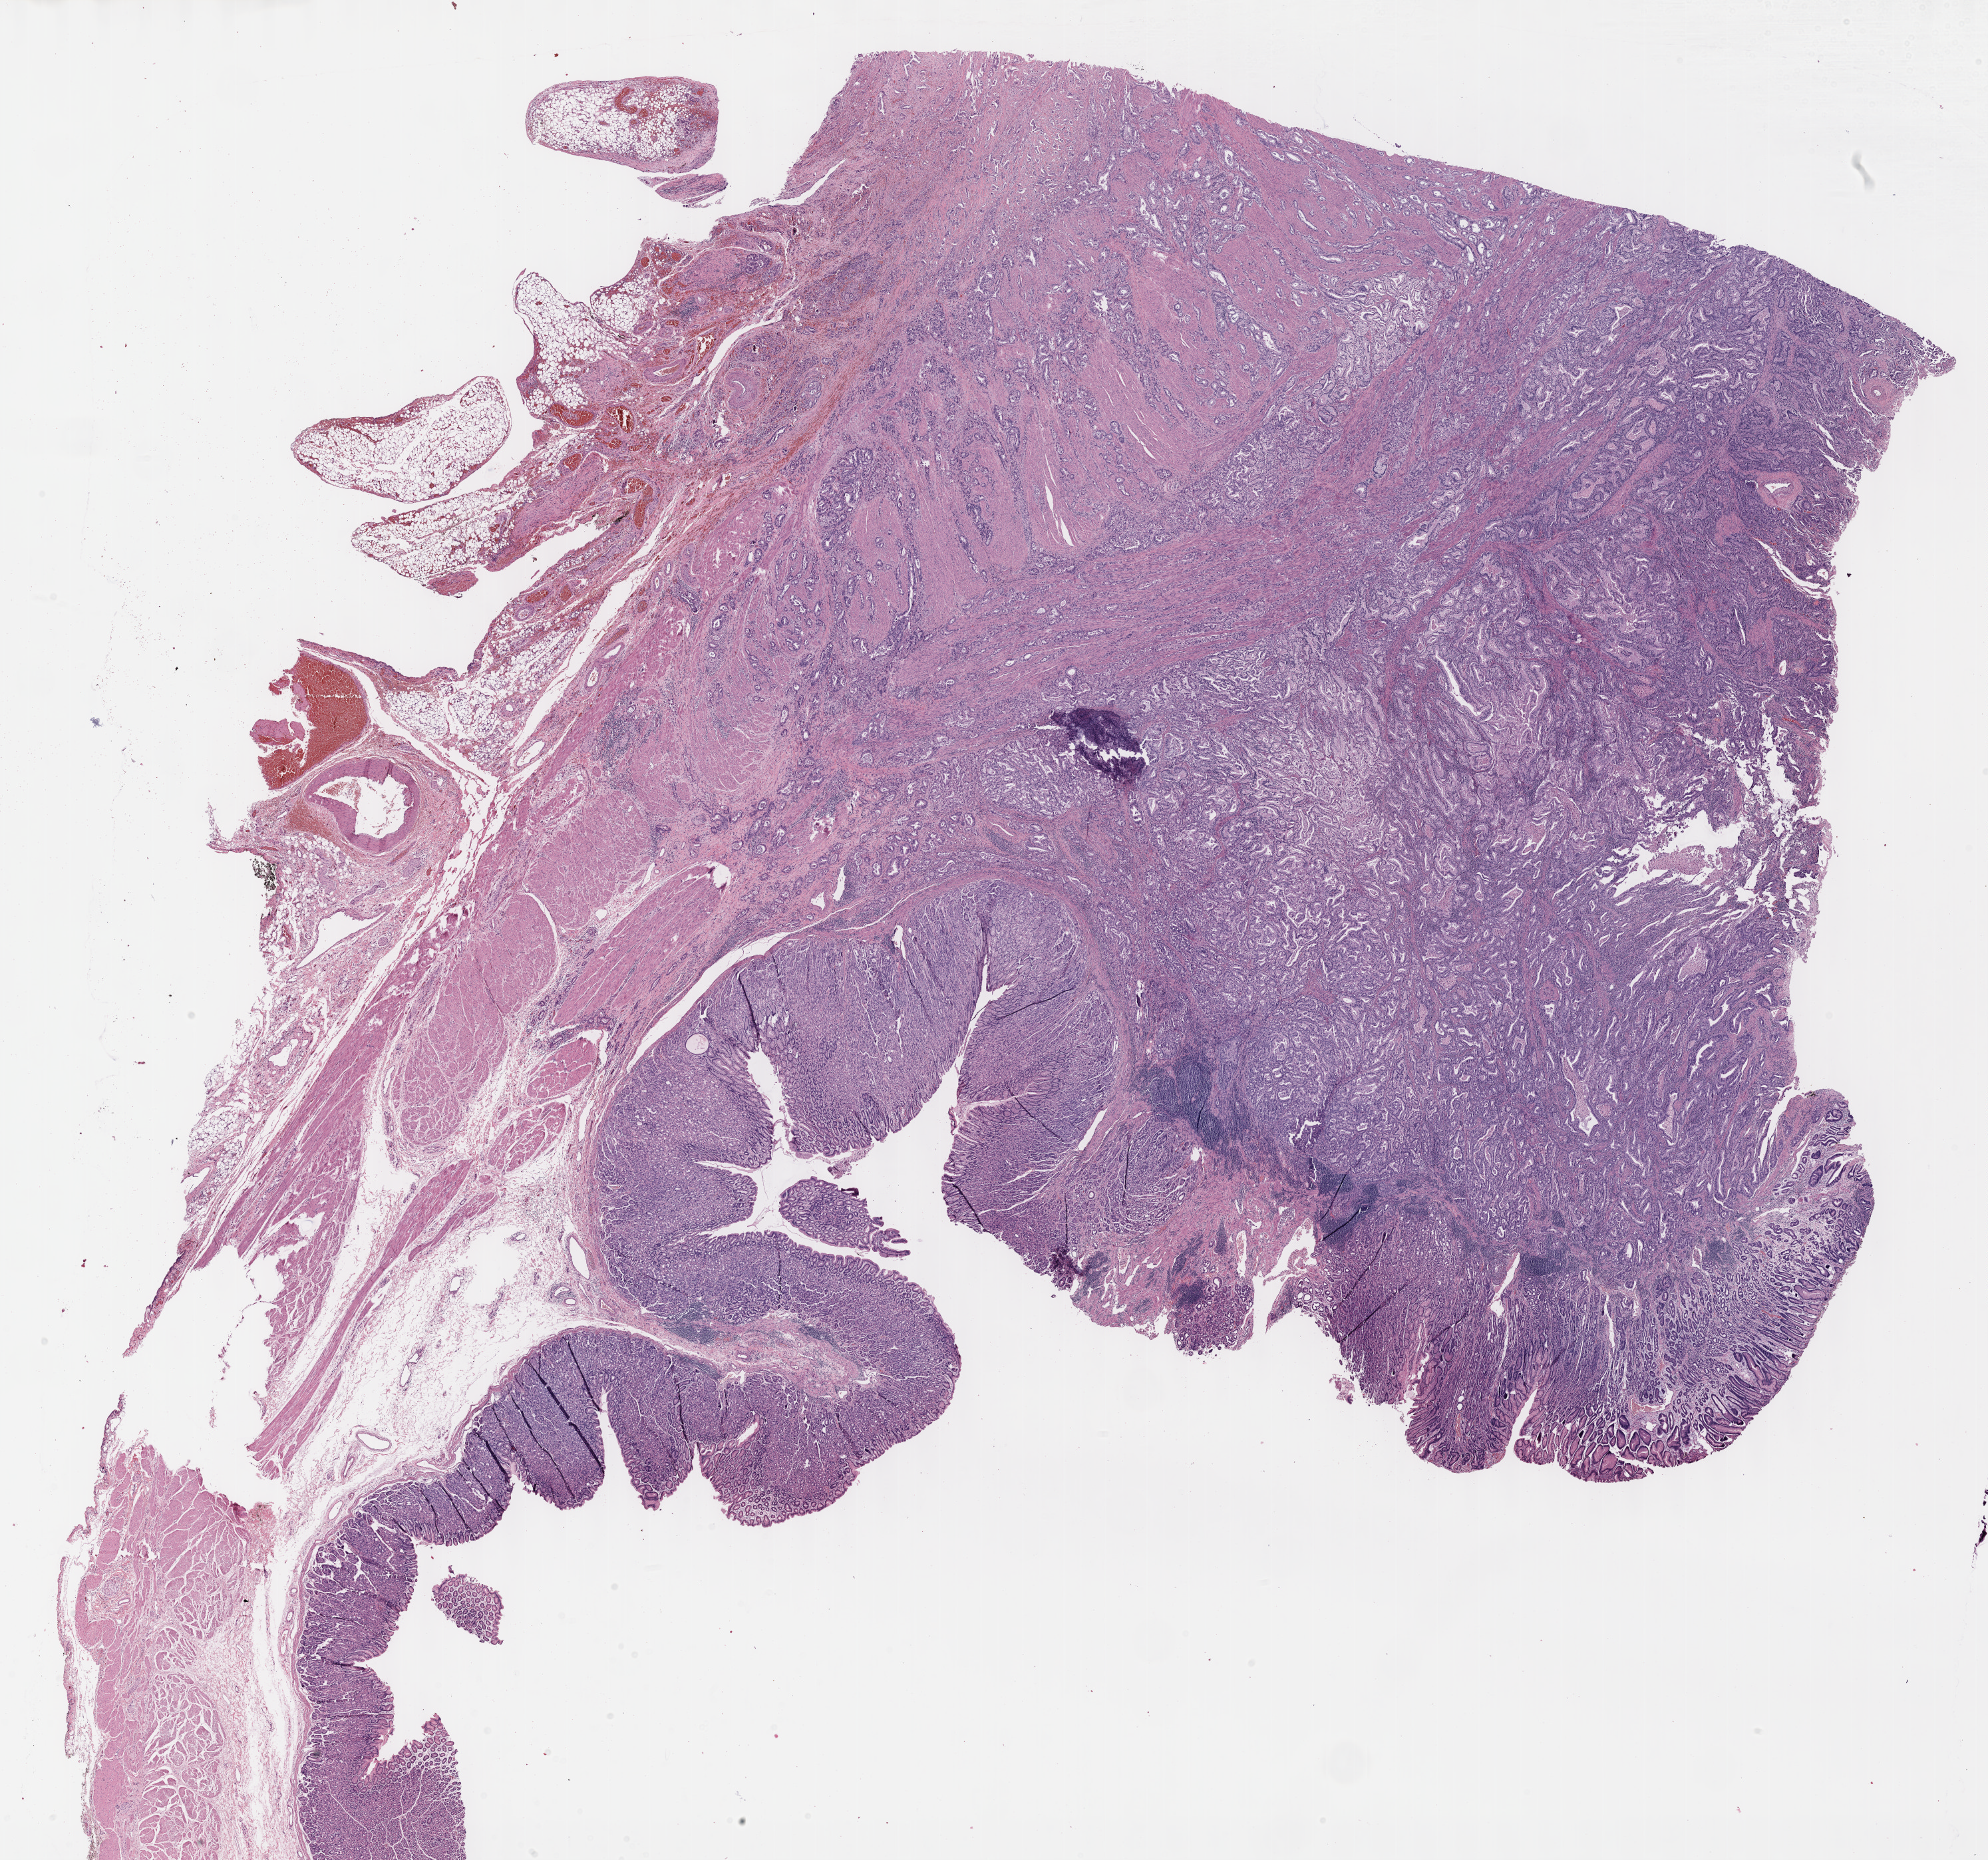
Digitized Hematoxylin and eosin (H&E) stained tissue section (whole slide), low-resolution overview of the scanned area, about 24.1 x 22.6 mm (from a 40x scan), FFPE section, stomach, primary tumour sample. Female, age 52 years at initial diagnosis. Histologic grade: G2 (moderately differentiated).
• pathologic diagnosis: Tubular adenocarcinoma (cardia, NOS)
• AJCC pathologic stage: IIIC
• TNM: T4a N3 M0